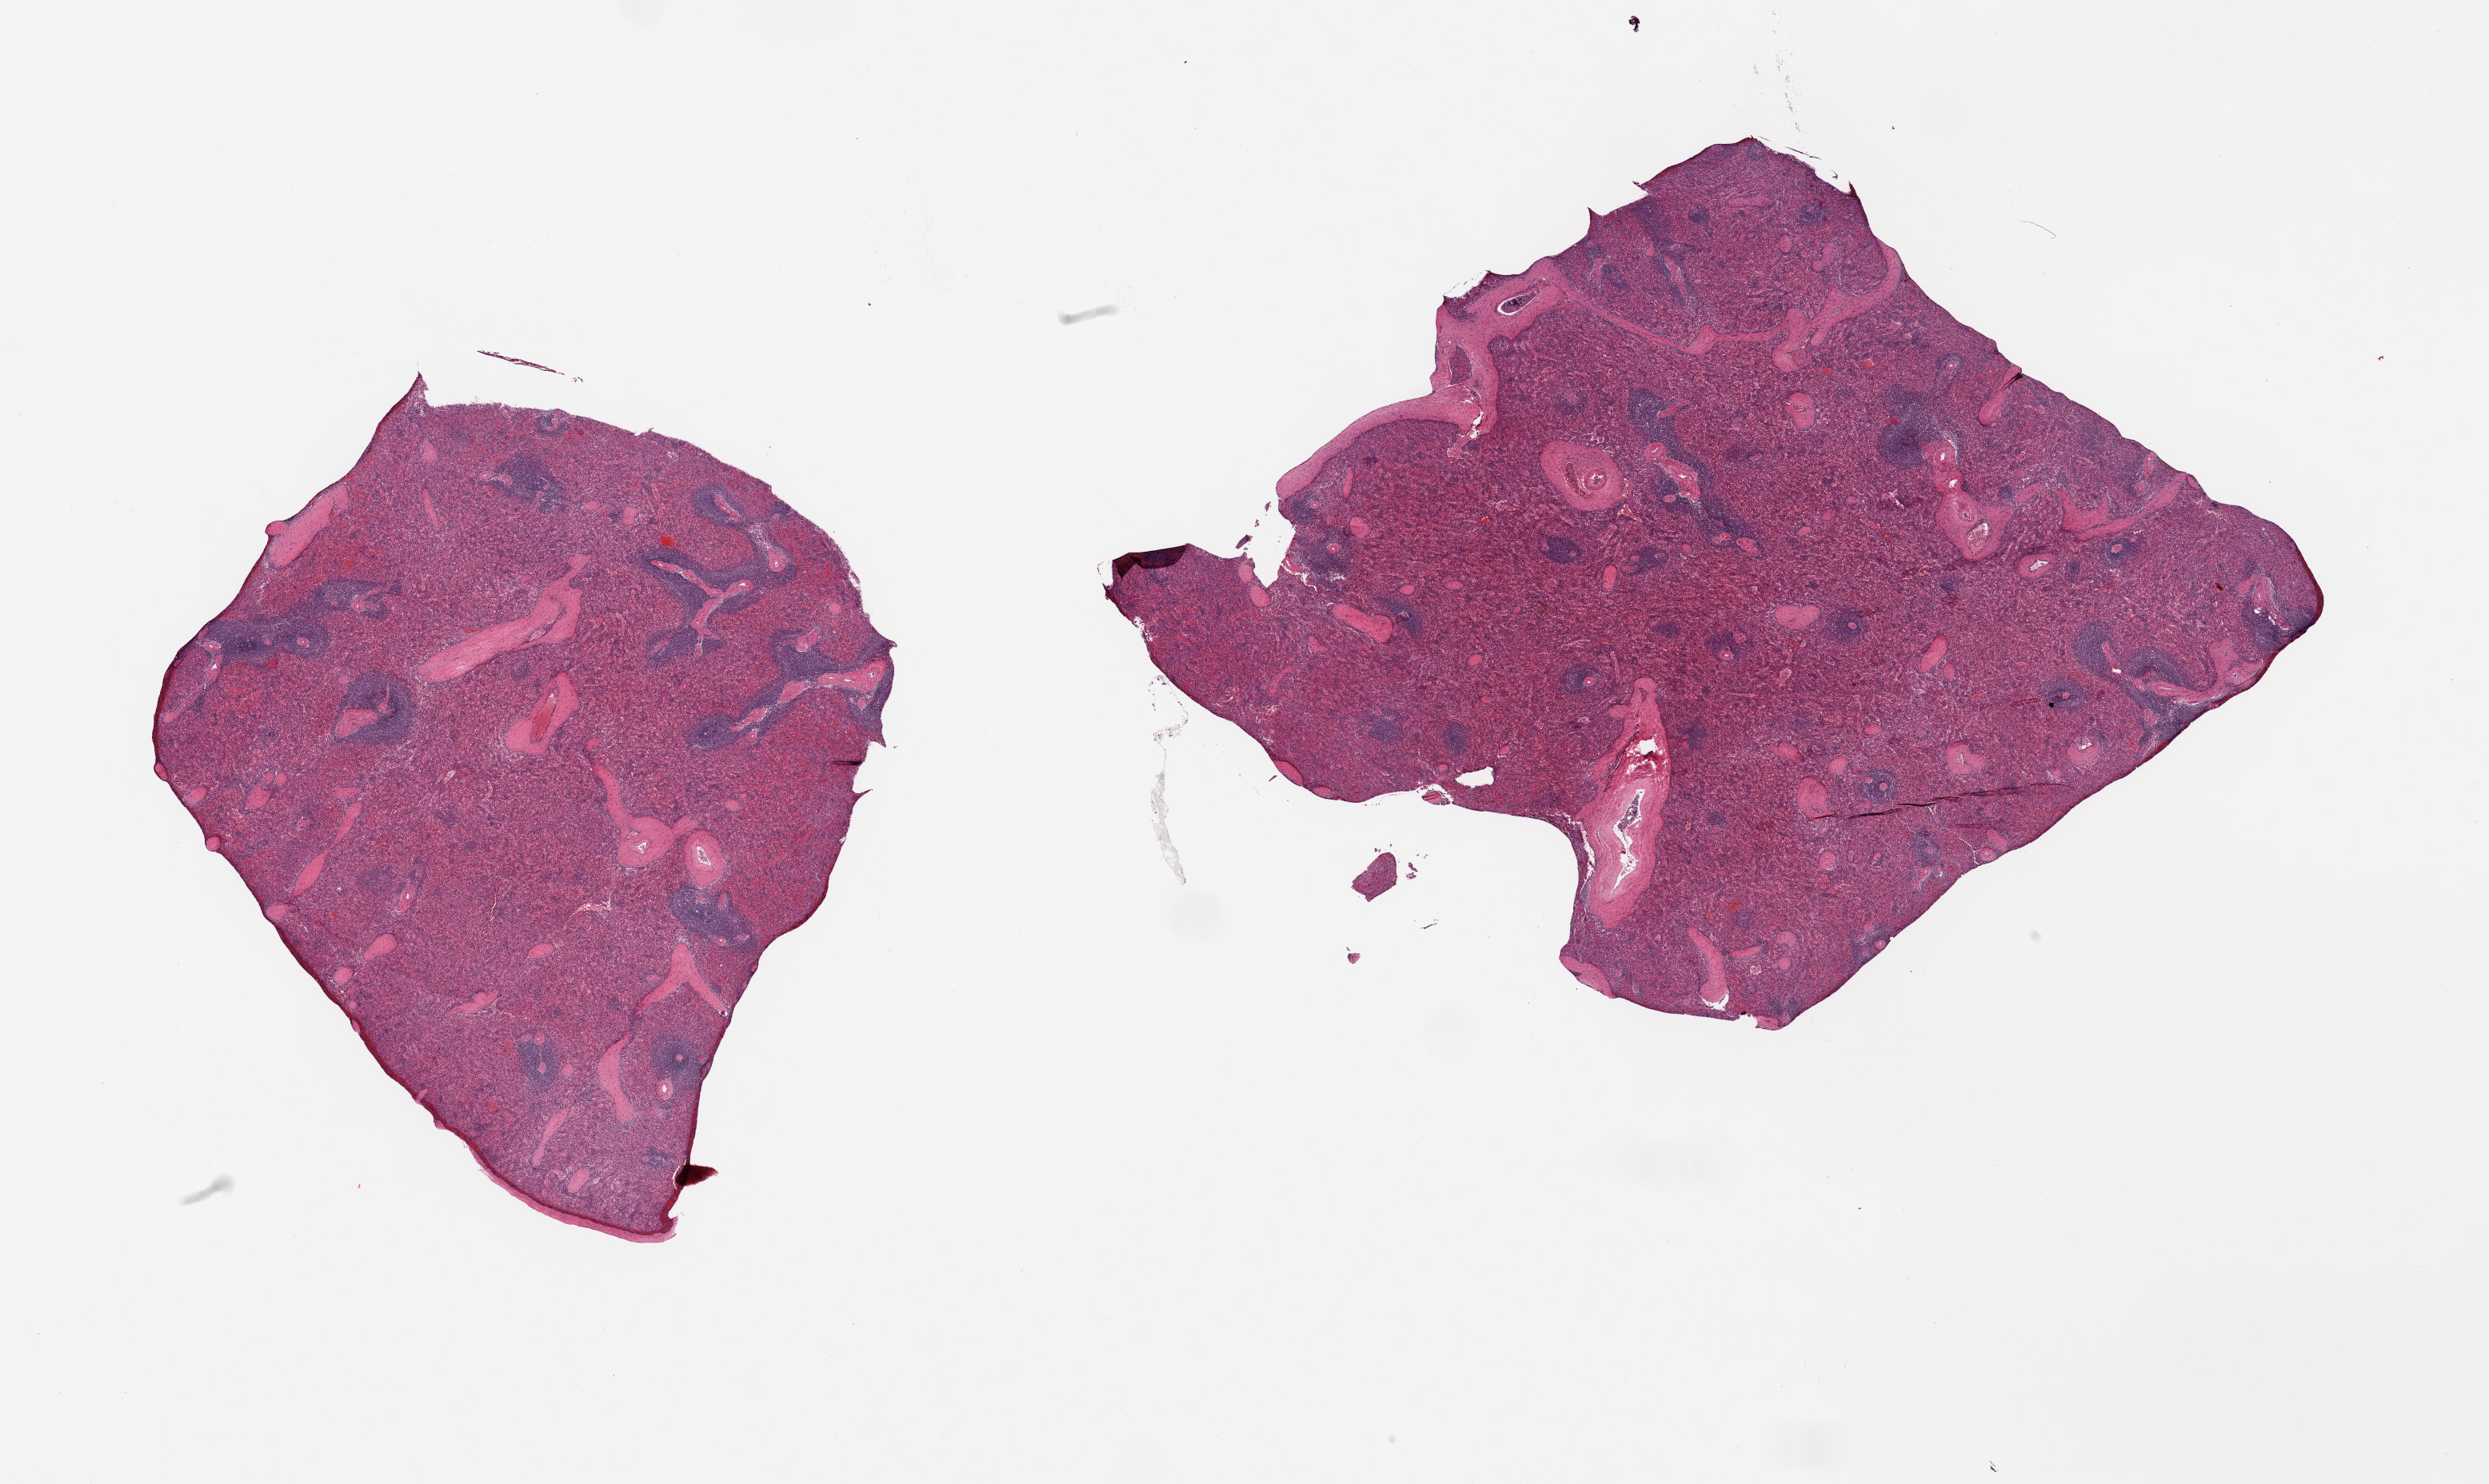
H&E whole-slide image — whole scanned area (about 24.6 x 14.7 mm, from a 20x scan) shown as a low-resolution overview, PAXgene-fixed paraffin-embedded (PFPE) section, section of spleen (target tissue), tissue donor sample. Male donor.
Pathologist's review note for this sample: 2 pieces, no abnormalities.